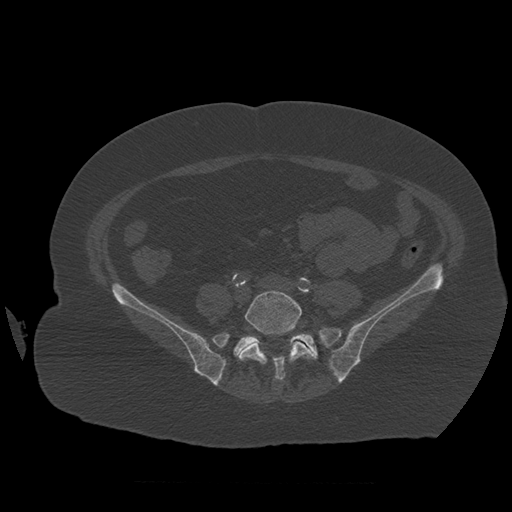
CT including the spine, one axial slice. Position 177 of 399 along the scan axis. Reconstruction kernel STANDARD. Bone window (W 1800 / L 400 HU). 512 × 512 image matrix. Patient age 81 years. Case-level facts recorded for this patient, not image findings: primary cancer: renal.
Outlined on this slice (semi-automatic segmentation, software-assisted and operator-edited):
- L5 vertebra: bounding box (x1, y1, x2, y2) in pixels: (239, 291, 314, 381)